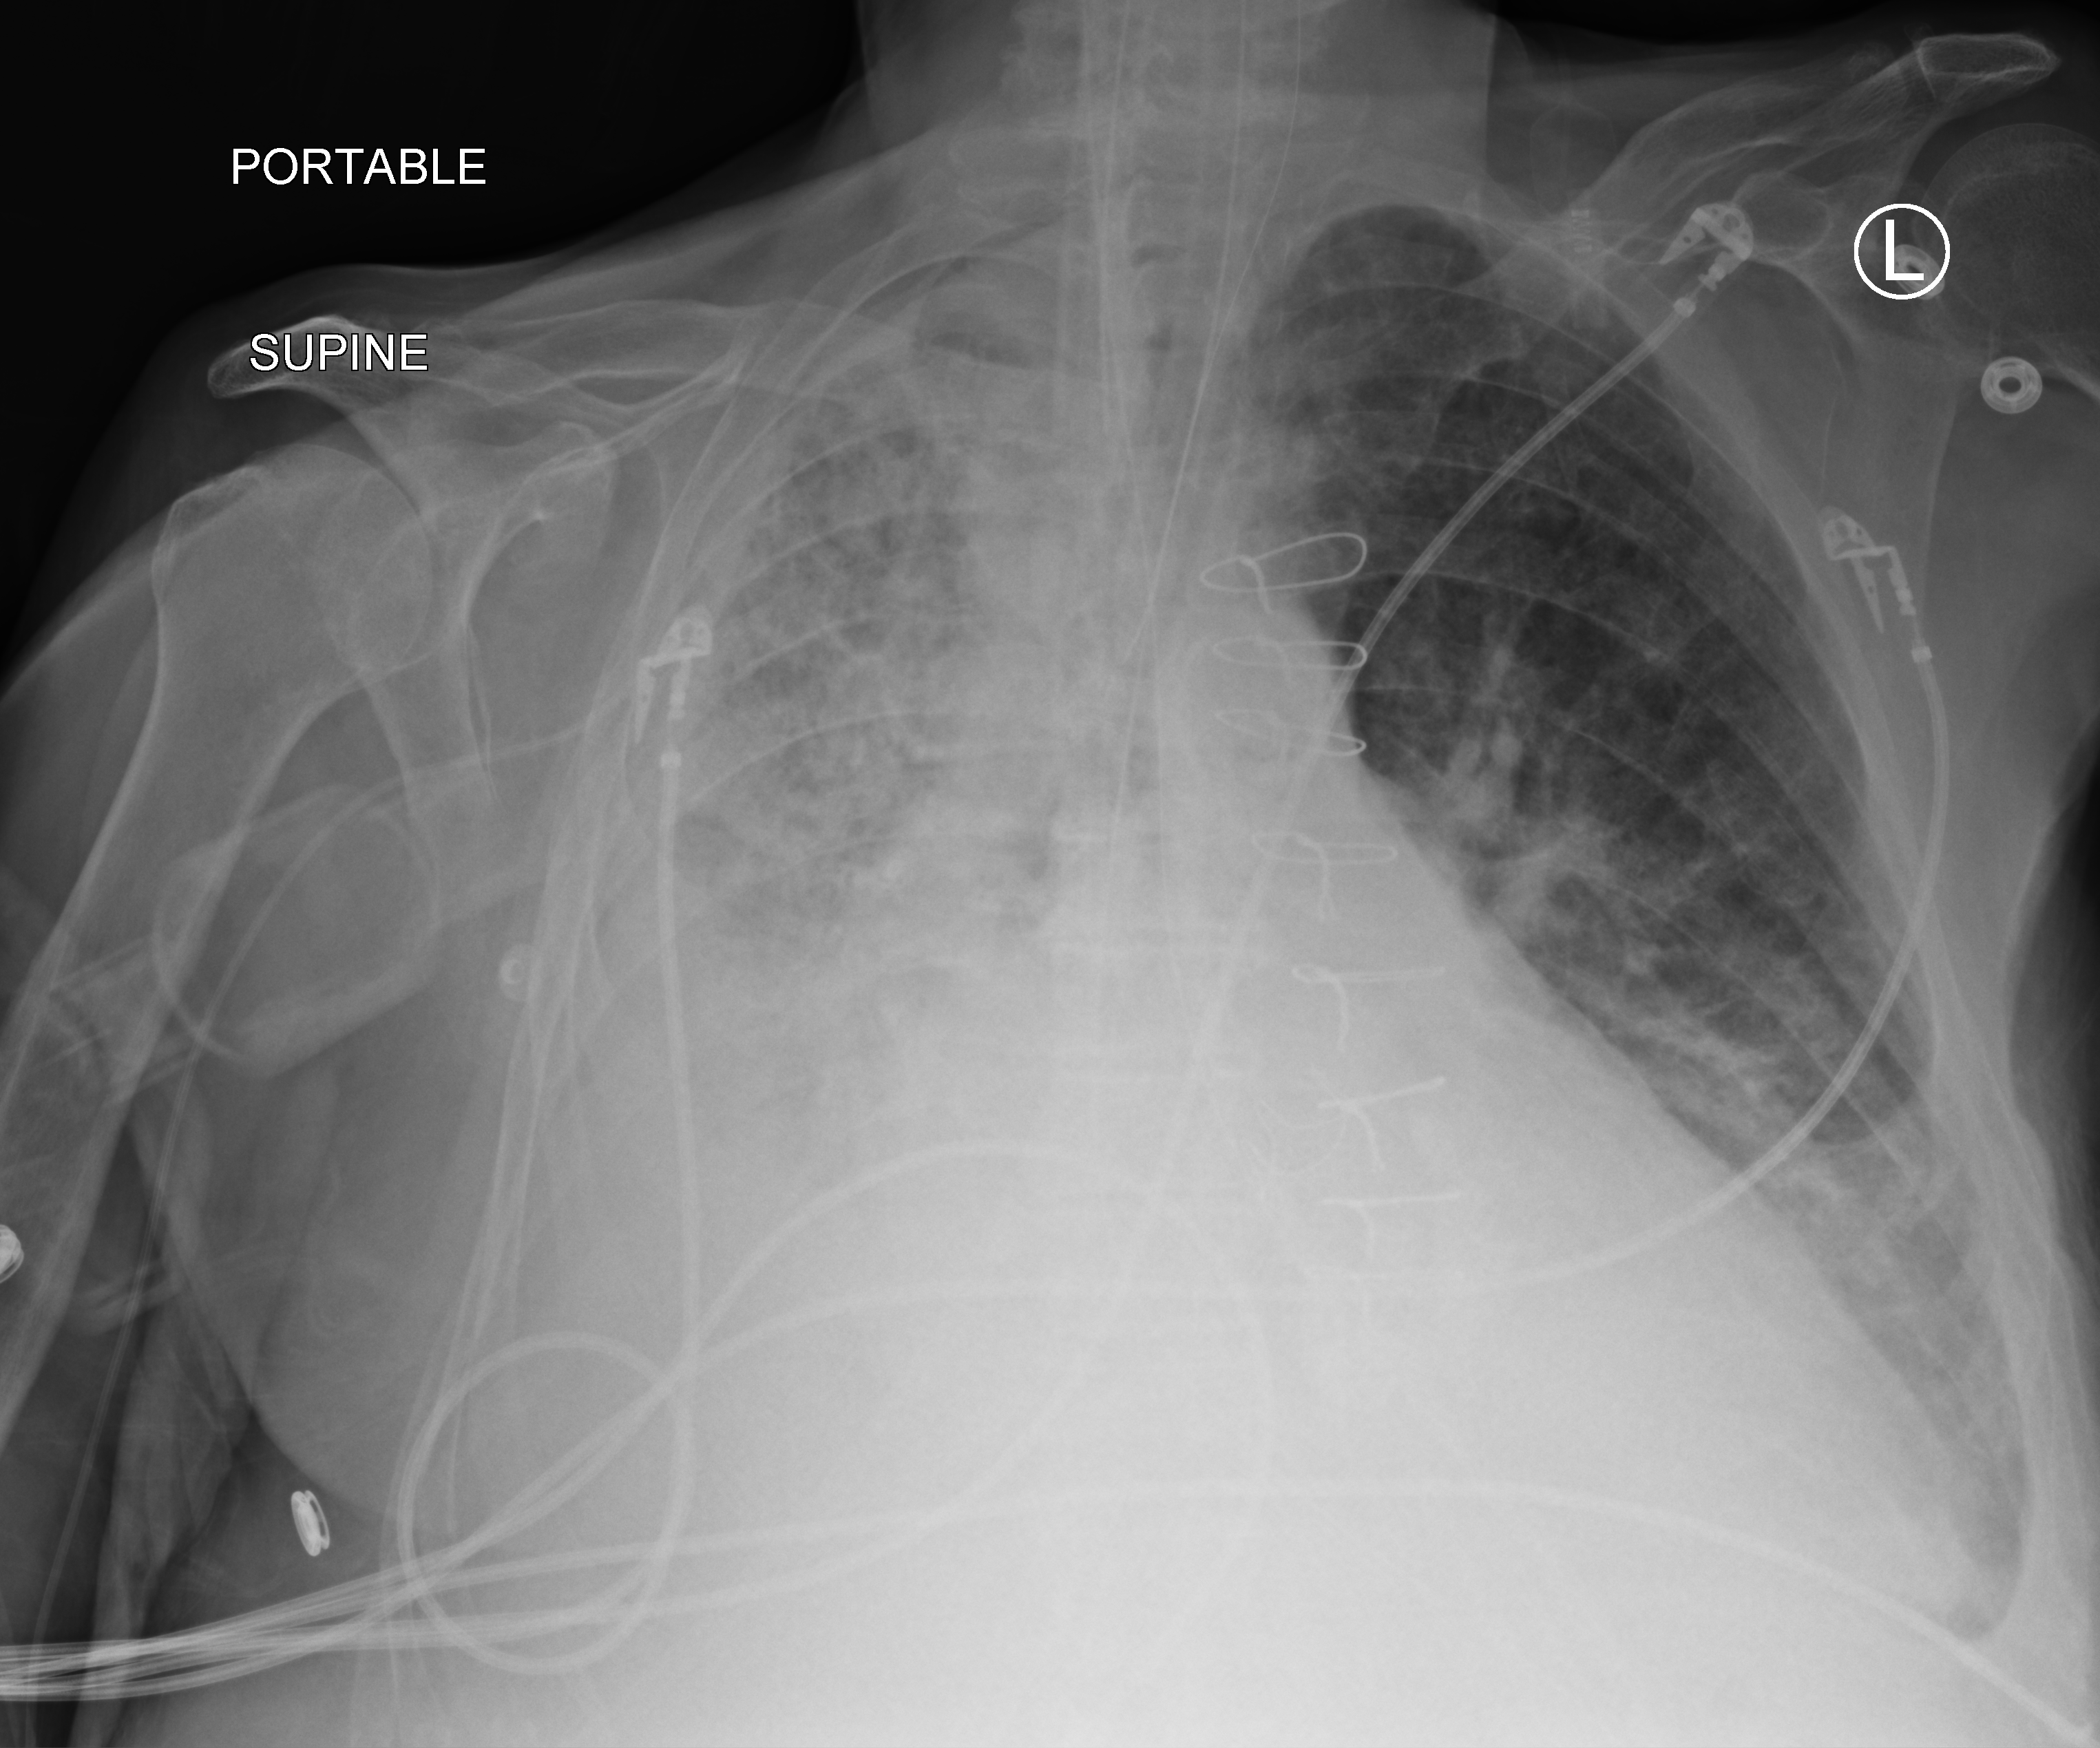
Chest X-ray (portable). Patient hospitalised with COVID-19; male, aged 75–90 years.
Hospital-stay facts (about this admission, not read from this image; timing relative to this image not recorded):
- mechanically ventilated during this hospital stay: yes
- admitted to intensive care during this hospital stay: yes
- length of hospital stay: 40 days